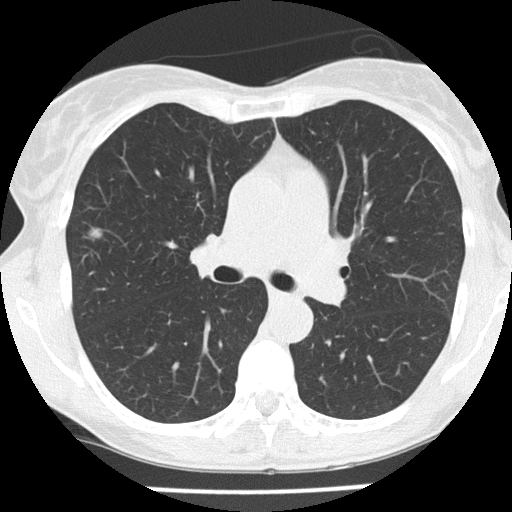
Axial slice from a low-dose chest CT screening exam. First (baseline) screen. Lung window (W 1500 / L -600 HU). Female participant, aged 56 years at enrolment. Former smoker at enrolment.
Lesion marked by an expert reader, bounding box <80,222,117,250> (left, top, right, bottom; pixels). Screening reader's record for this exam (one nodule recorded; not confirmed to be the boxed lesion): non-calcified nodule or mass ≥4 mm, right upper lobe, 7 × 5 mm, poorly defined margins, ground glass attenuation. Official screen result: positive, change unspecified: nodule(s) >= 4 mm or enlarging nodule(s), mass(es), or other non-specific abnormalities suspicious for lung cancer. Lung cancer was diagnosed 148 days after this screen: bronchiolo-alveolar carcinoma, non-mucinous, right upper lobe, well differentiated (G1), stage IA (AJCC 6th edition), 6 mm at pathology.